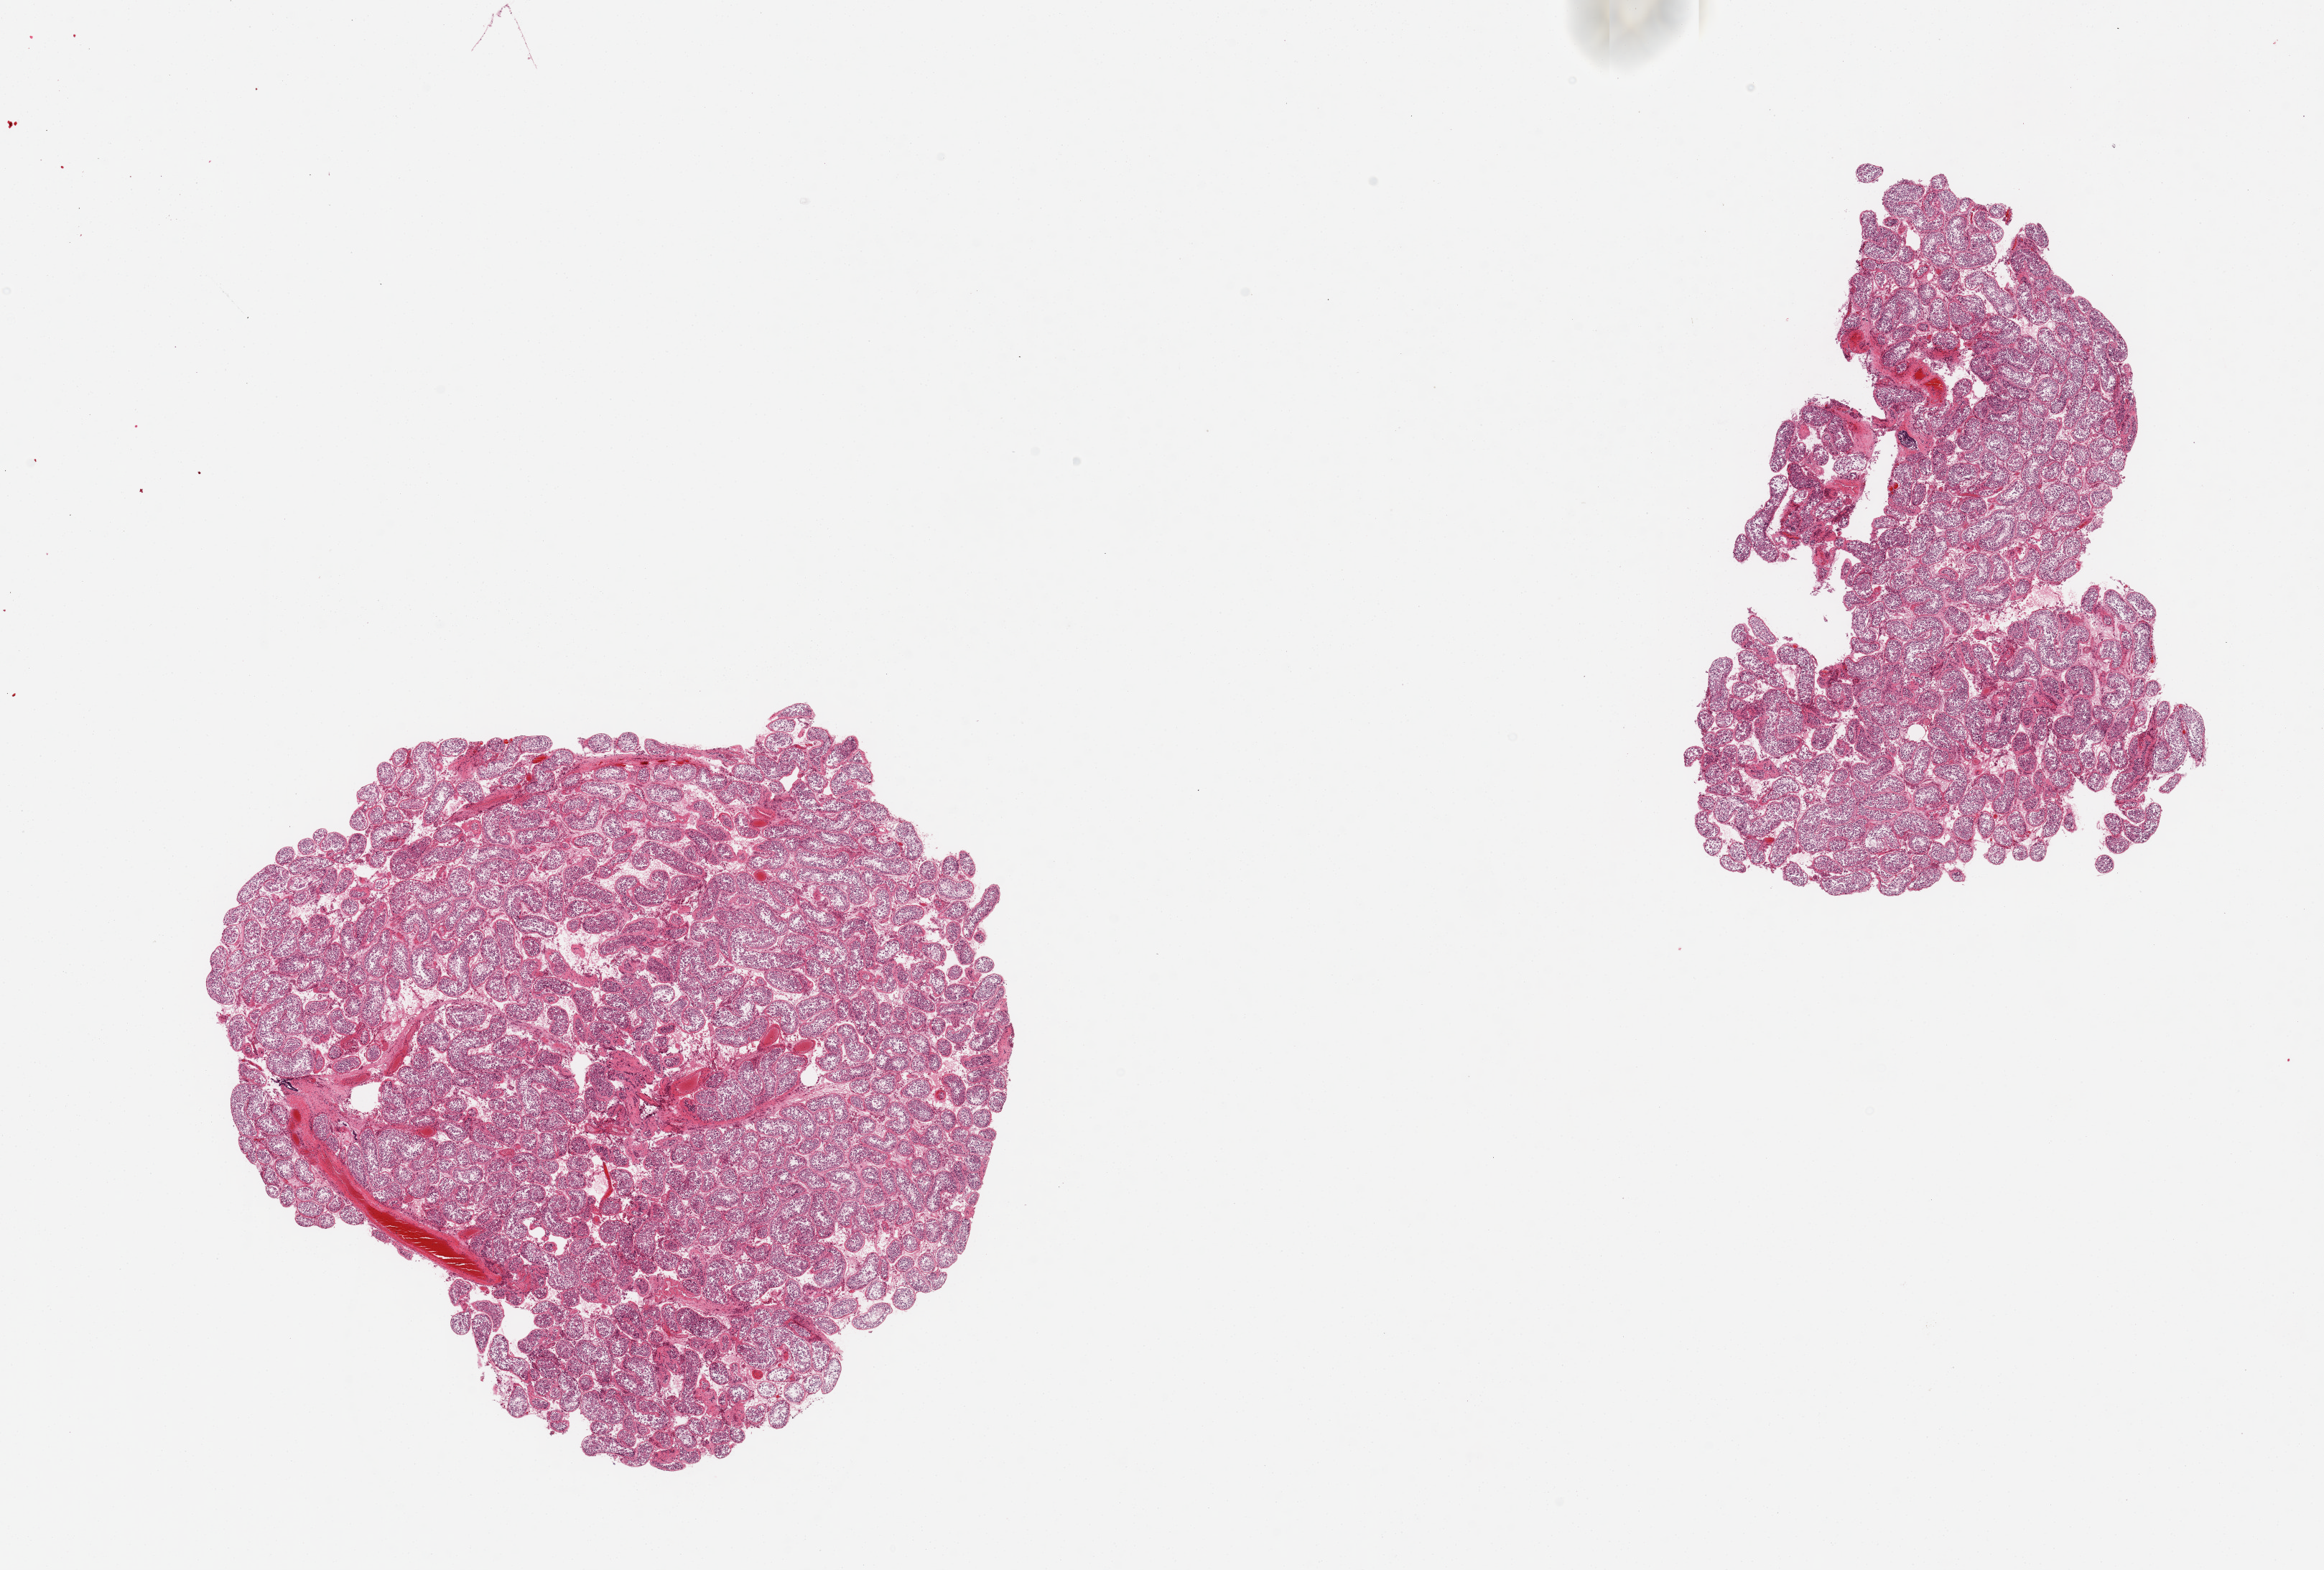
Haematoxylin and eosin whole-slide image, brightfield — shown as a low-resolution overview of the whole scanned area (about 25.6 x 17.3 mm, acquisition: 20x scan). PAXgene-fixed, paraffin-embedded tissue. Target tissue: testis. Donor tissue sample. Donor: male.
Pathologist's review note for this sample: 2 pieces; spermatogenesis.